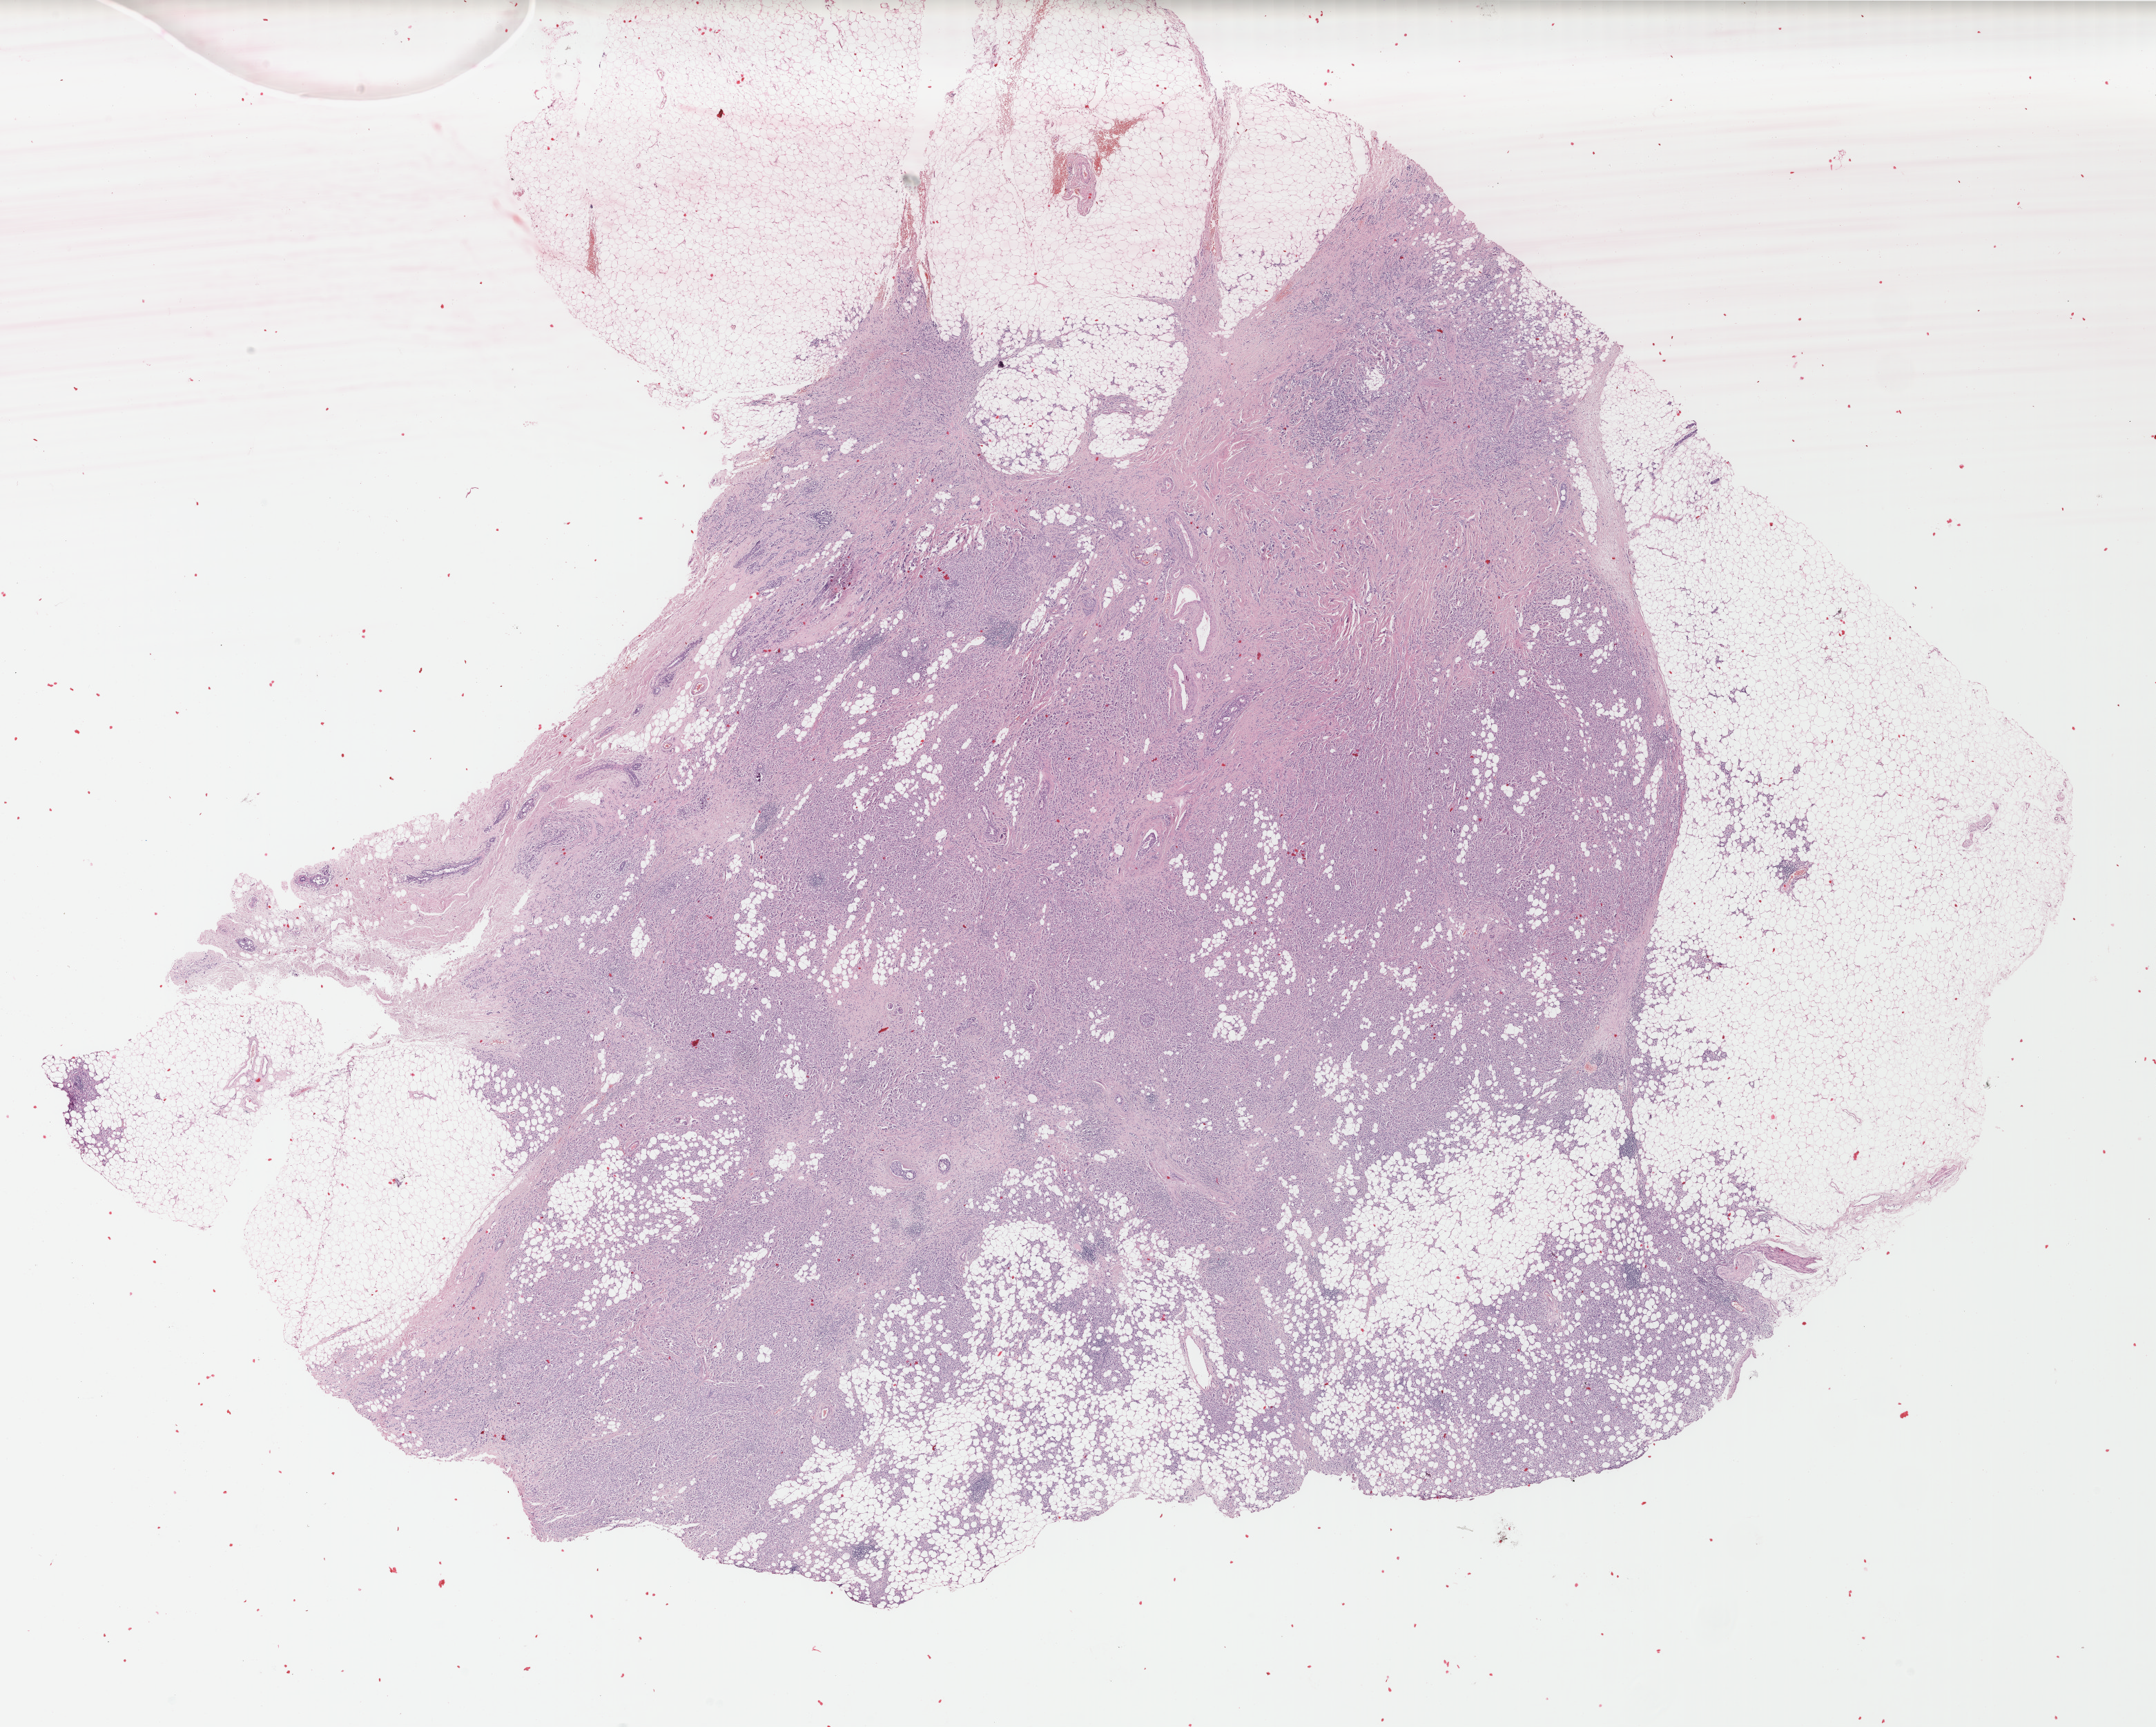
Whole-slide histology image, H&E, a low-resolution overview of the entire scanned area, about 24.8 x 19.9 mm, formalin-fixed paraffin-embedded (FFPE) diagnostic section, sample: primary tumour, breast. Female, age 80 years at initial diagnosis.
AJCC pathologic stage: IIA. Lymph nodes positive (case pathology): 1 of 7 examined. Histologic diagnosis: Infiltrating duct carcinoma, NOS.